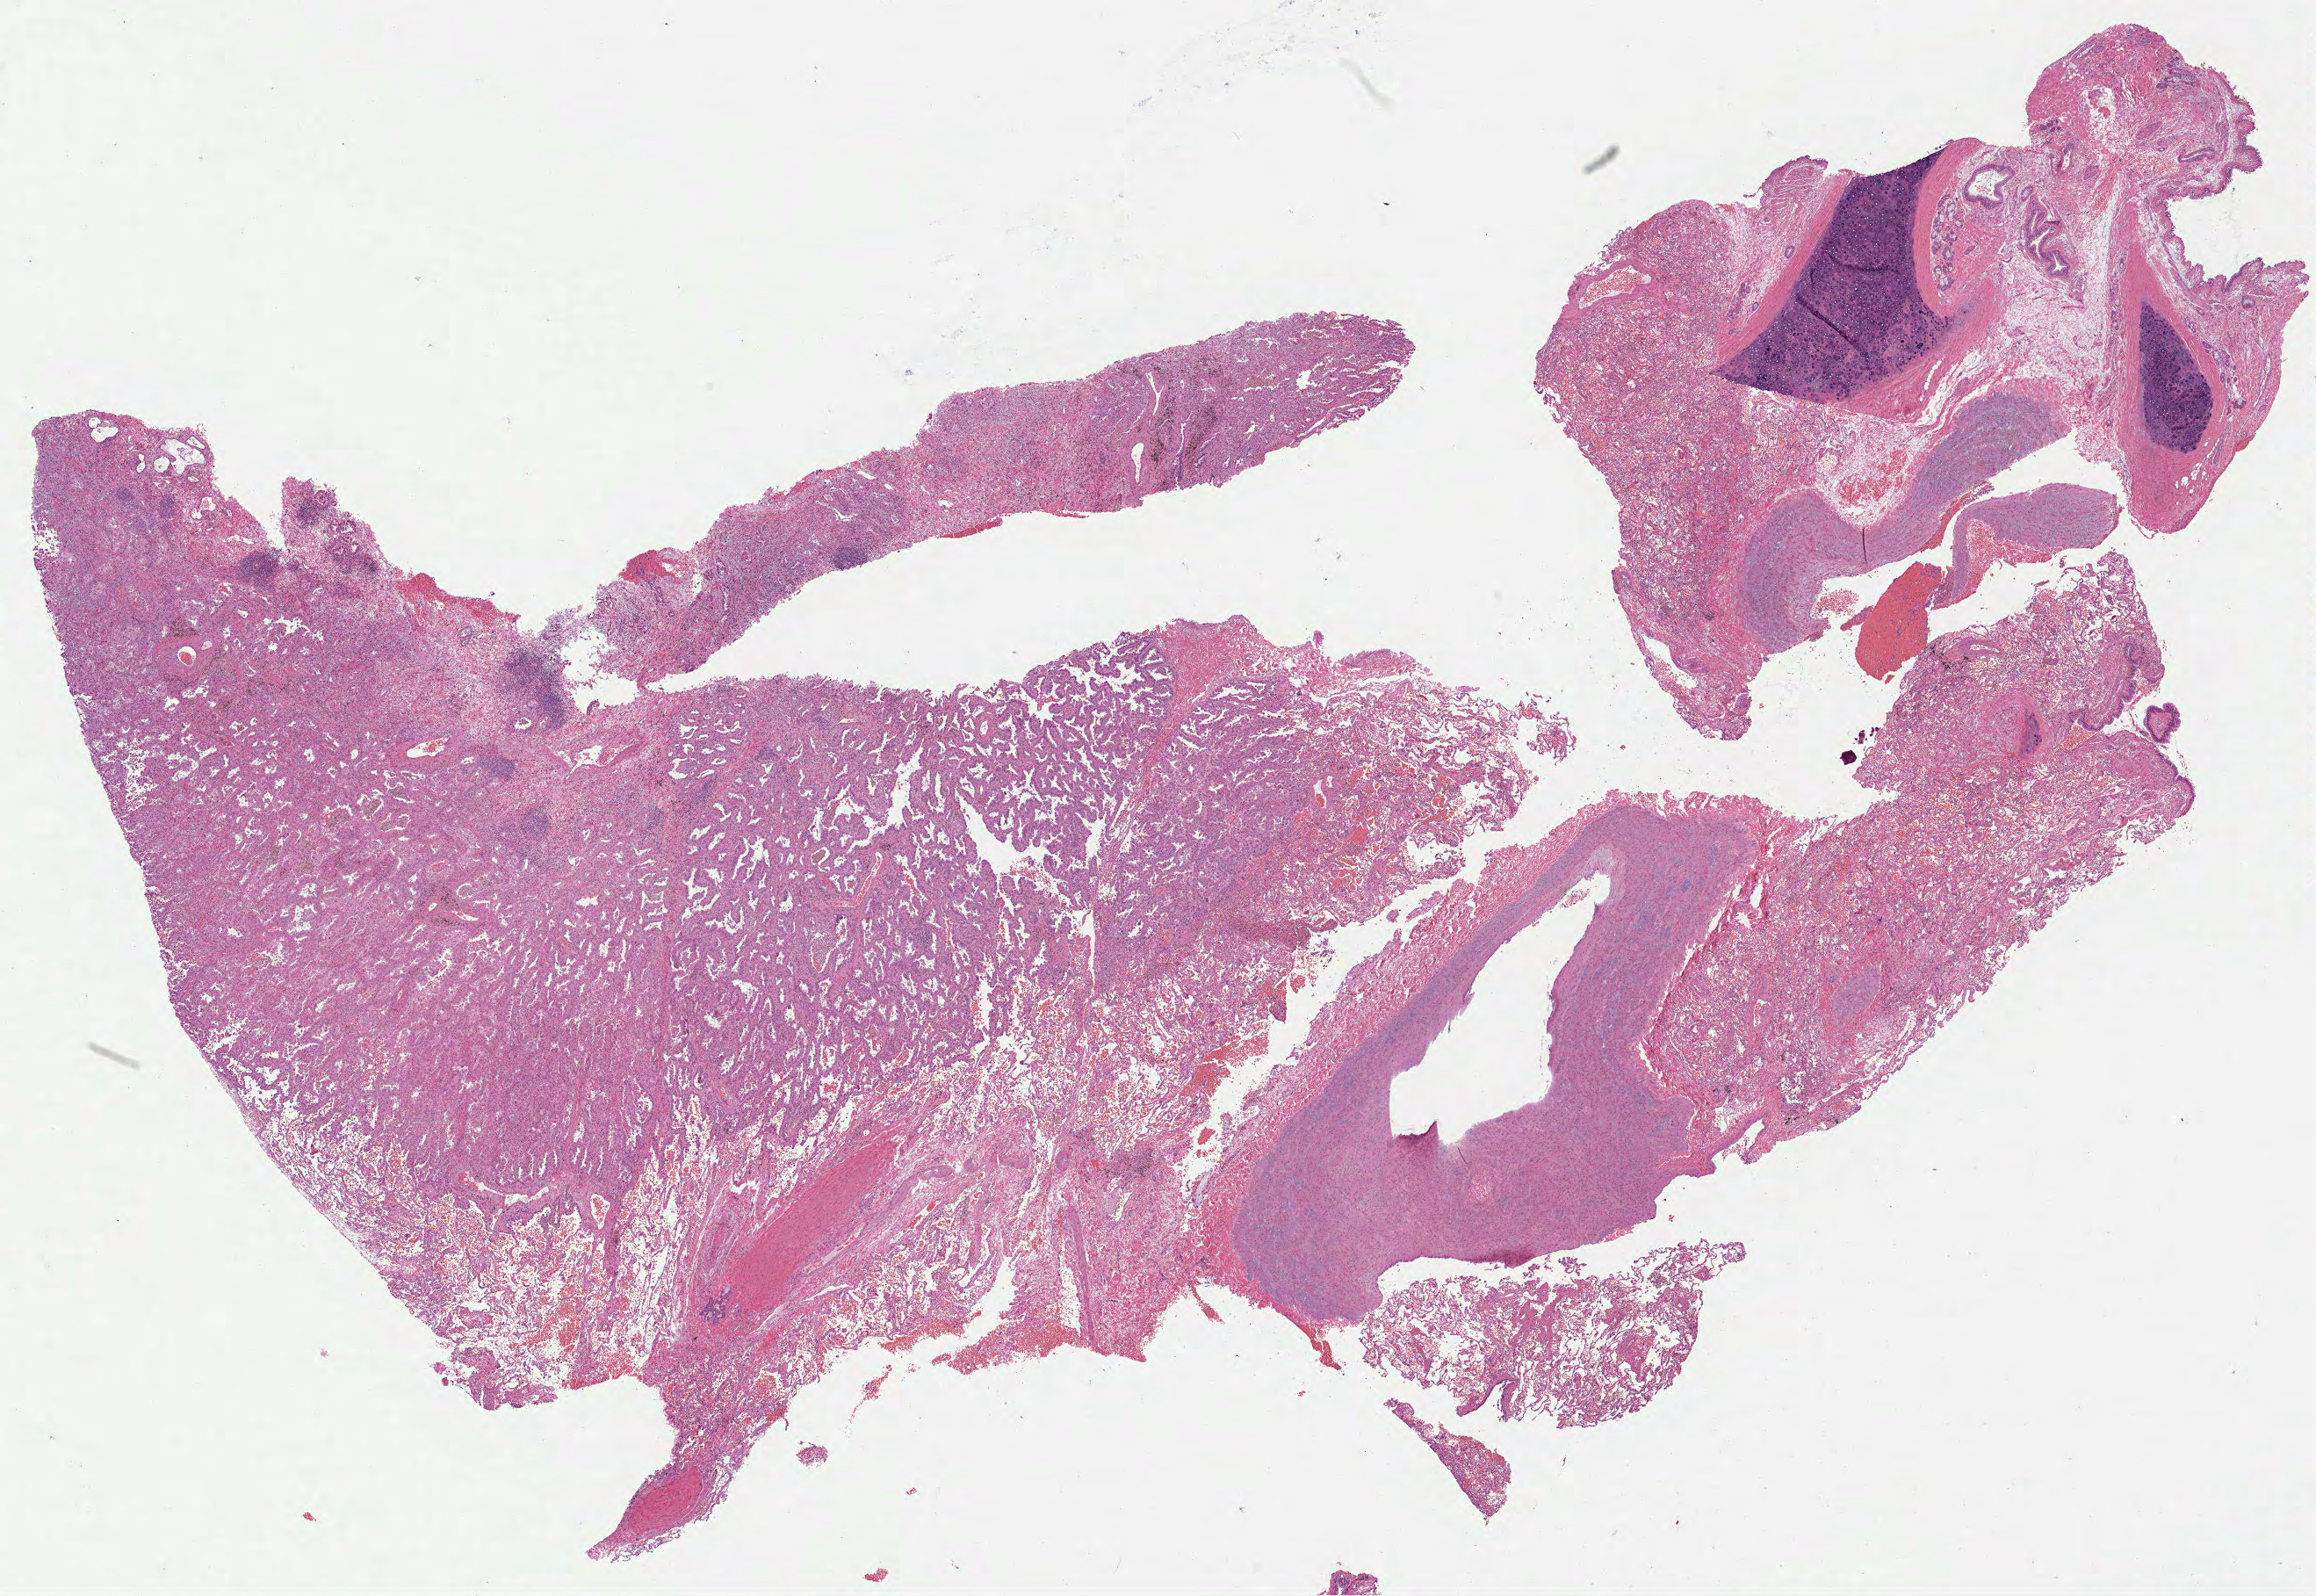
Whole-slide histology image, Hematoxylin and eosin (H&E) stained, a low-resolution overview of the entire scanned area, about 21.3 x 14.7 mm (slide scanned at 40x); formalin-fixed paraffin-embedded (FFPE) diagnostic section; sample: primary tumour, lung. Female patient; age at initial diagnosis 70 years.
Pathologic diagnosis: Adenocarcinoma, NOS (upper lobe, lung). AJCC pathologic stage: IB (7th edition). TNM: T2a N0 MX.